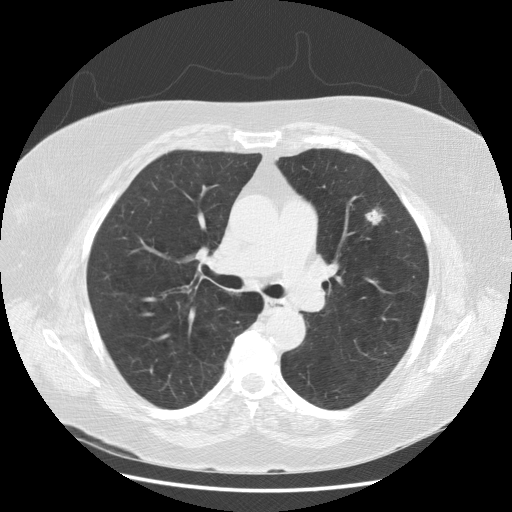
Axial slice from a low-dose chest CT screening exam; second annual screen; lung window (W 1500 / L -600 HU); 2.5 mm slice thickness; 120 kVp; 512 × 512 image matrix. Female participant, aged 68 years at enrolment. Current smoker at enrolment.
Lesion marked by an expert reader, bounding box [x1, y1, x2, y2] px = [360, 200, 397, 233]. The screening reader recorded 2 non-calcified nodules or masses ≥4 mm on this exam (left upper lobe, right upper lobe); which of them this box marks is not recorded. Participant outcome: lung cancer diagnosed 90 days after this screen — large cell carcinoma, NOS, left upper lobe, undifferentiated (G4), stage IA (AJCC 6th edition), 10 mm at pathology.